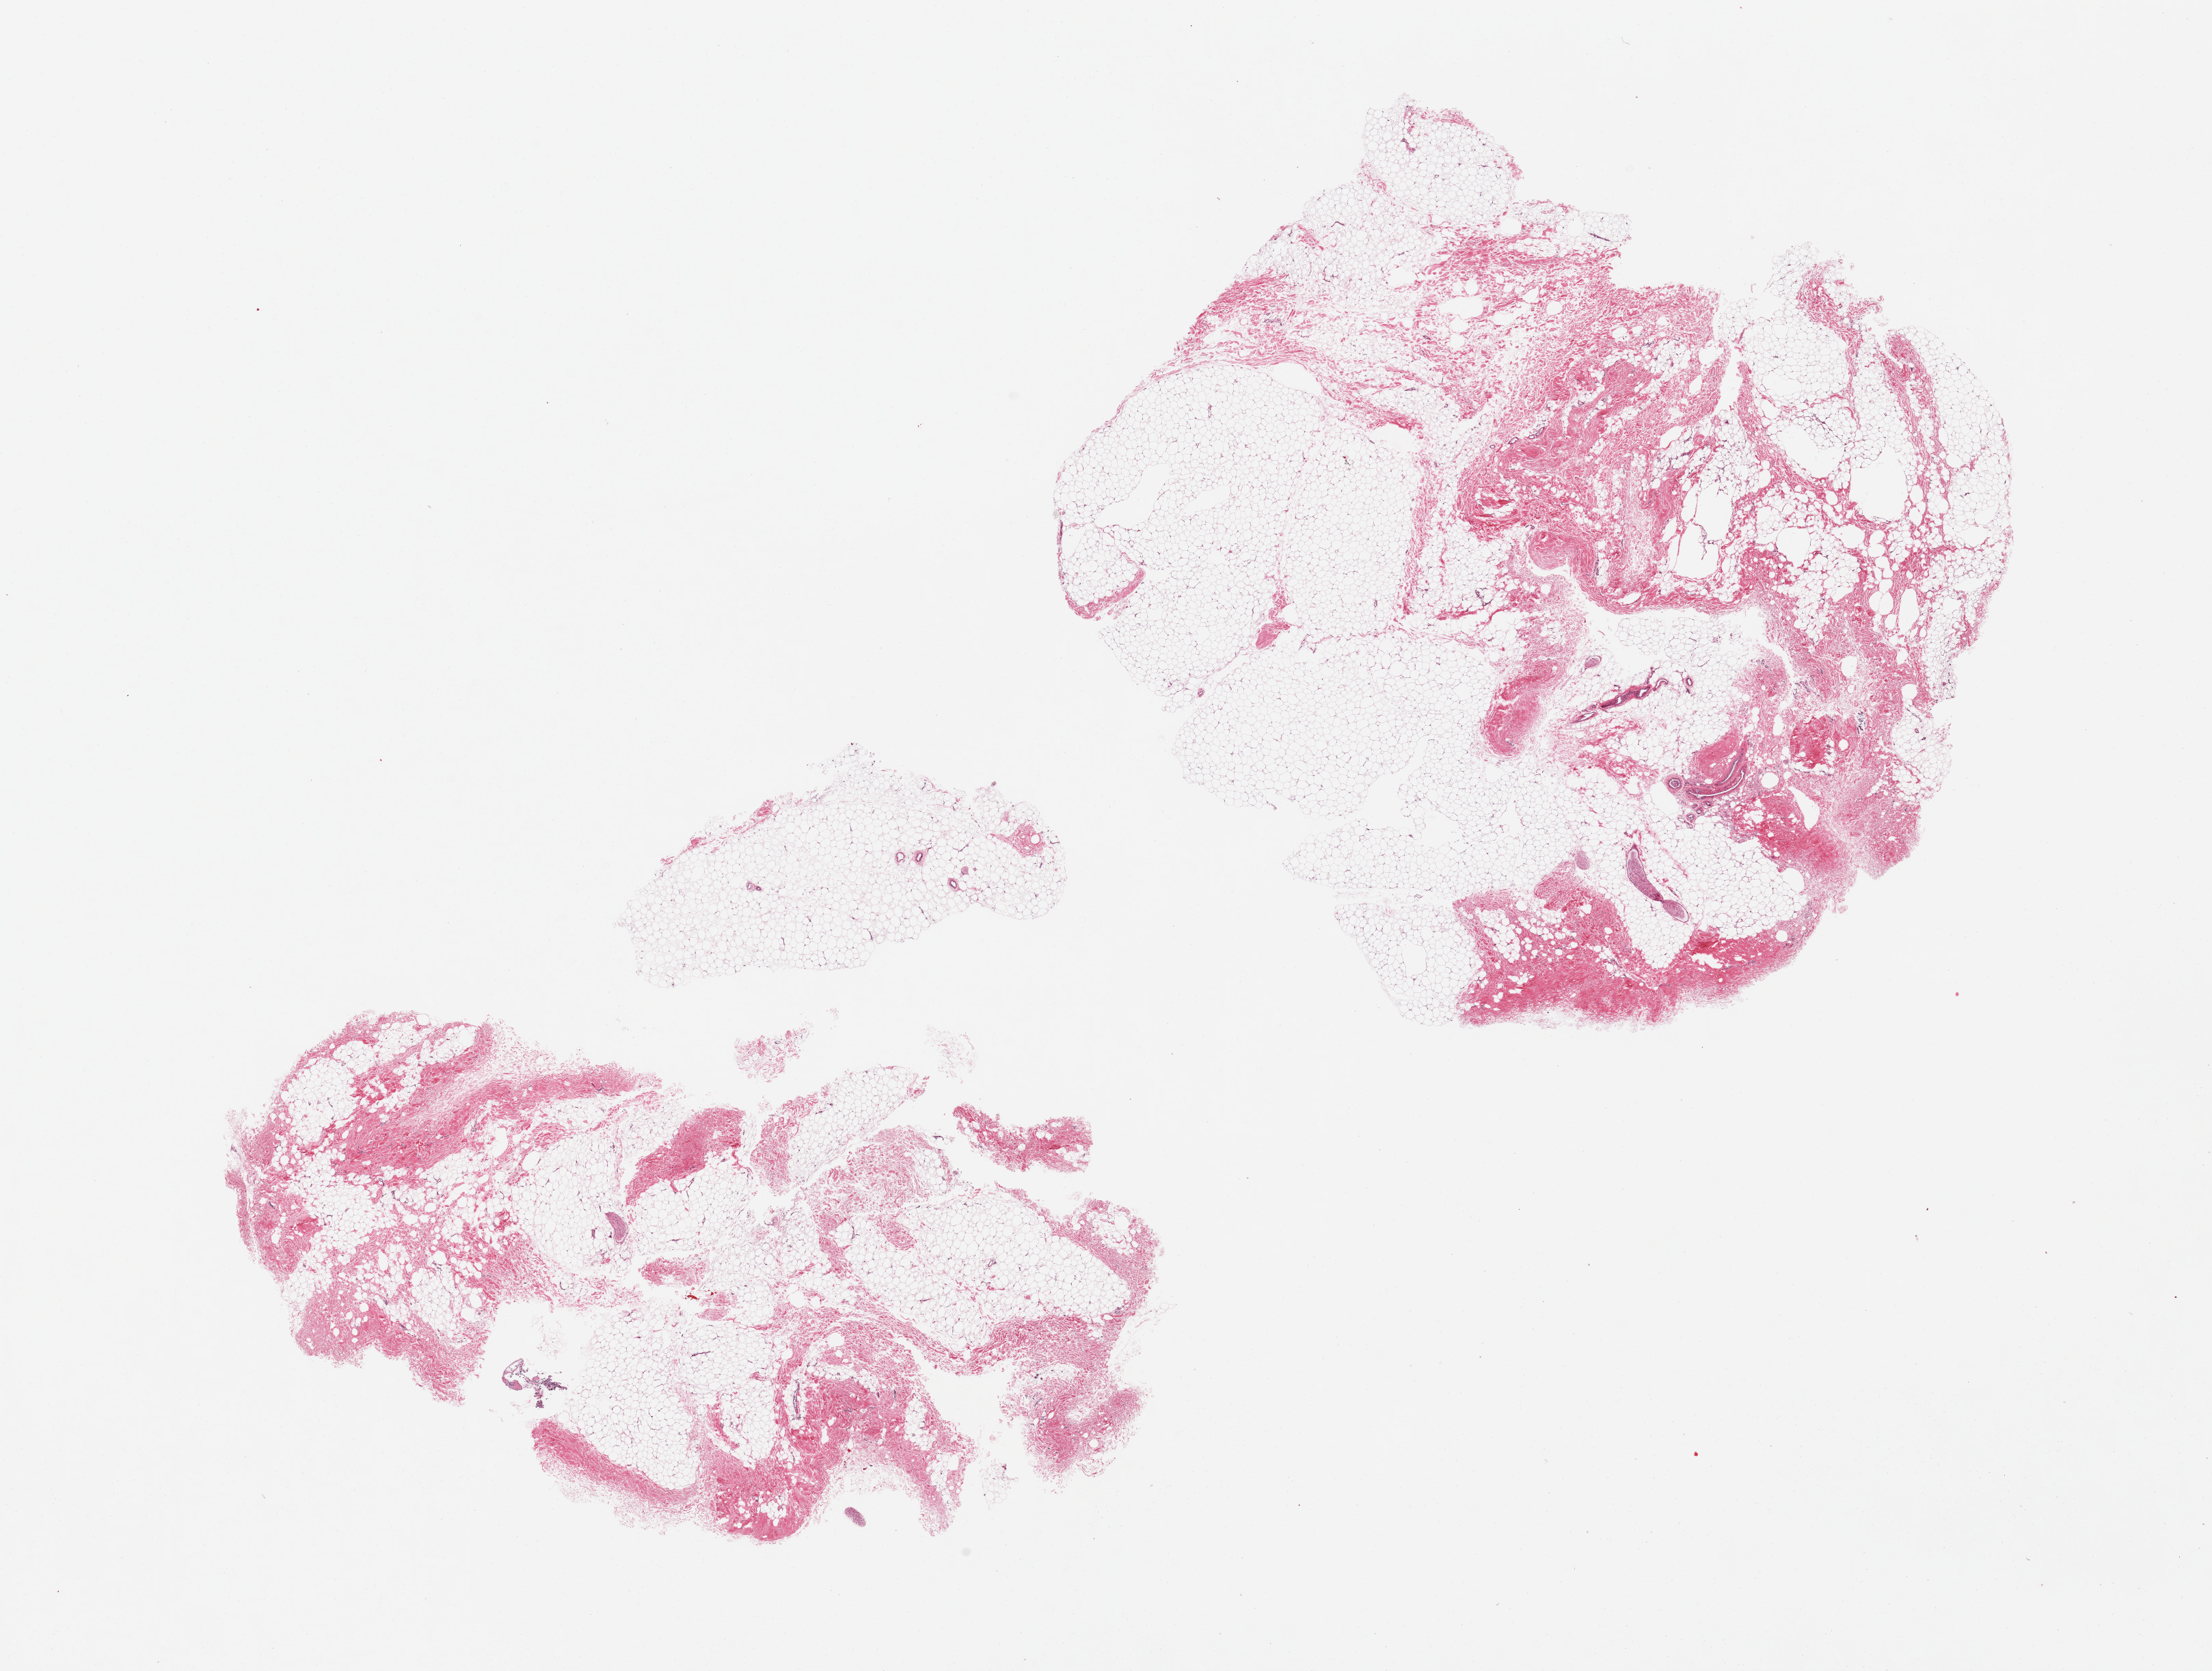
H&E whole-slide image, brightfield — low-resolution overview of the scanned area, about 25.6 x 19.3 mm (from a 20x scan); PAXgene-fixed, paraffin-embedded tissue; target tissue: breast; tissue donor sample. Donor: male.
Pathologist's review note for this sample: 2 pieces; fibrofatty tissue, no ductal elements noted.